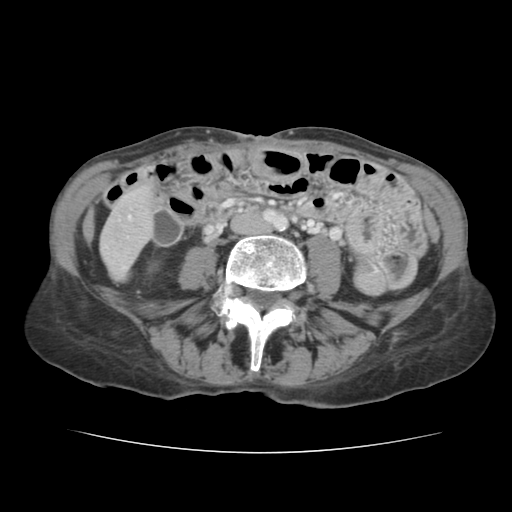
Contrast-enhanced abdominal CT, one axial slice. Slice 20 of 136 in the series (ordered by position). Soft-tissue window (W 400 / L 40 HU). 512 × 512 image matrix, field of view 319 × 319 mm. Female patient, age 77 years. From the clinical record (not read from this slice): diagnosis: colorectal cancer liver metastases, imaged before liver resection; multiple liver metastases: yes; largest metastasis: 3 cm.
Outlined on this slice (expert manual segmentation):
- liver: box from (x=102, y=189) to (x=151, y=276) px